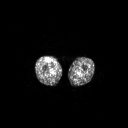
FDG PET of an extremity soft-tissue mass (from a PET/CT study), one axial slice; 3.27 mm slice thickness; 128 × 128 image matrix. Patient: male, 56 years. Case-level facts recorded for this patient, not image findings: histological type: pleiomorphic leiomyosarcoma; grade: intermediate; site of the primary tumour: right thigh.
Outlined on this slice (expert contour drawn on MRI and transferred to this co-registered scan by the dataset authors):
- gross tumour volume including surrounding oedema: bounding box [x1, y1, x2, y2] px = [46, 58, 51, 62]